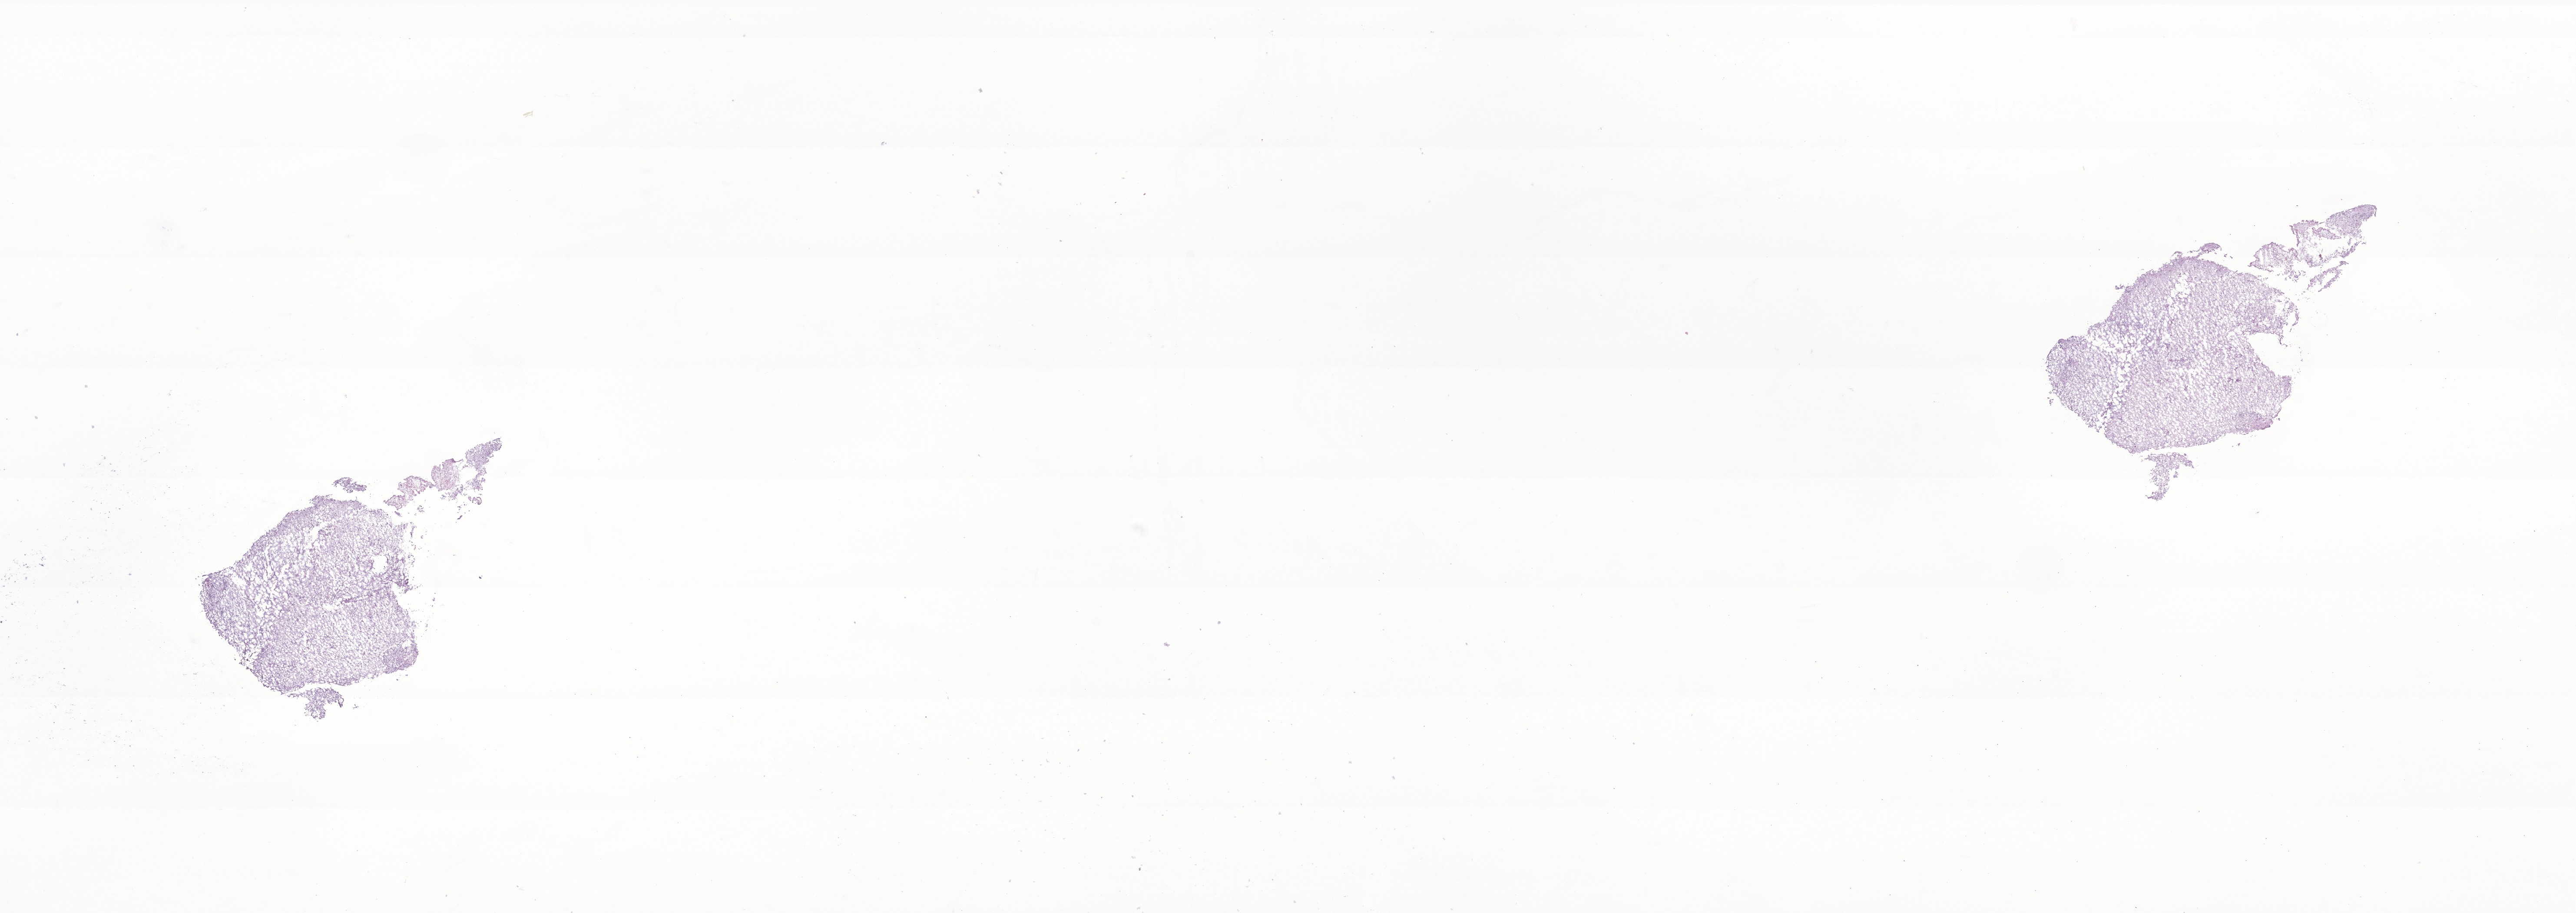
Haematoxylin and eosin whole-slide image of tumor tissue from the brain — shown as a low-resolution overview of the whole scanned area (about 25.0 x 8.9 mm), frozen section. Patient: male, age 187 months (15 years 7 months).
Recorded diagnosis: Neoplasm, uncertain whether benign or malignant.